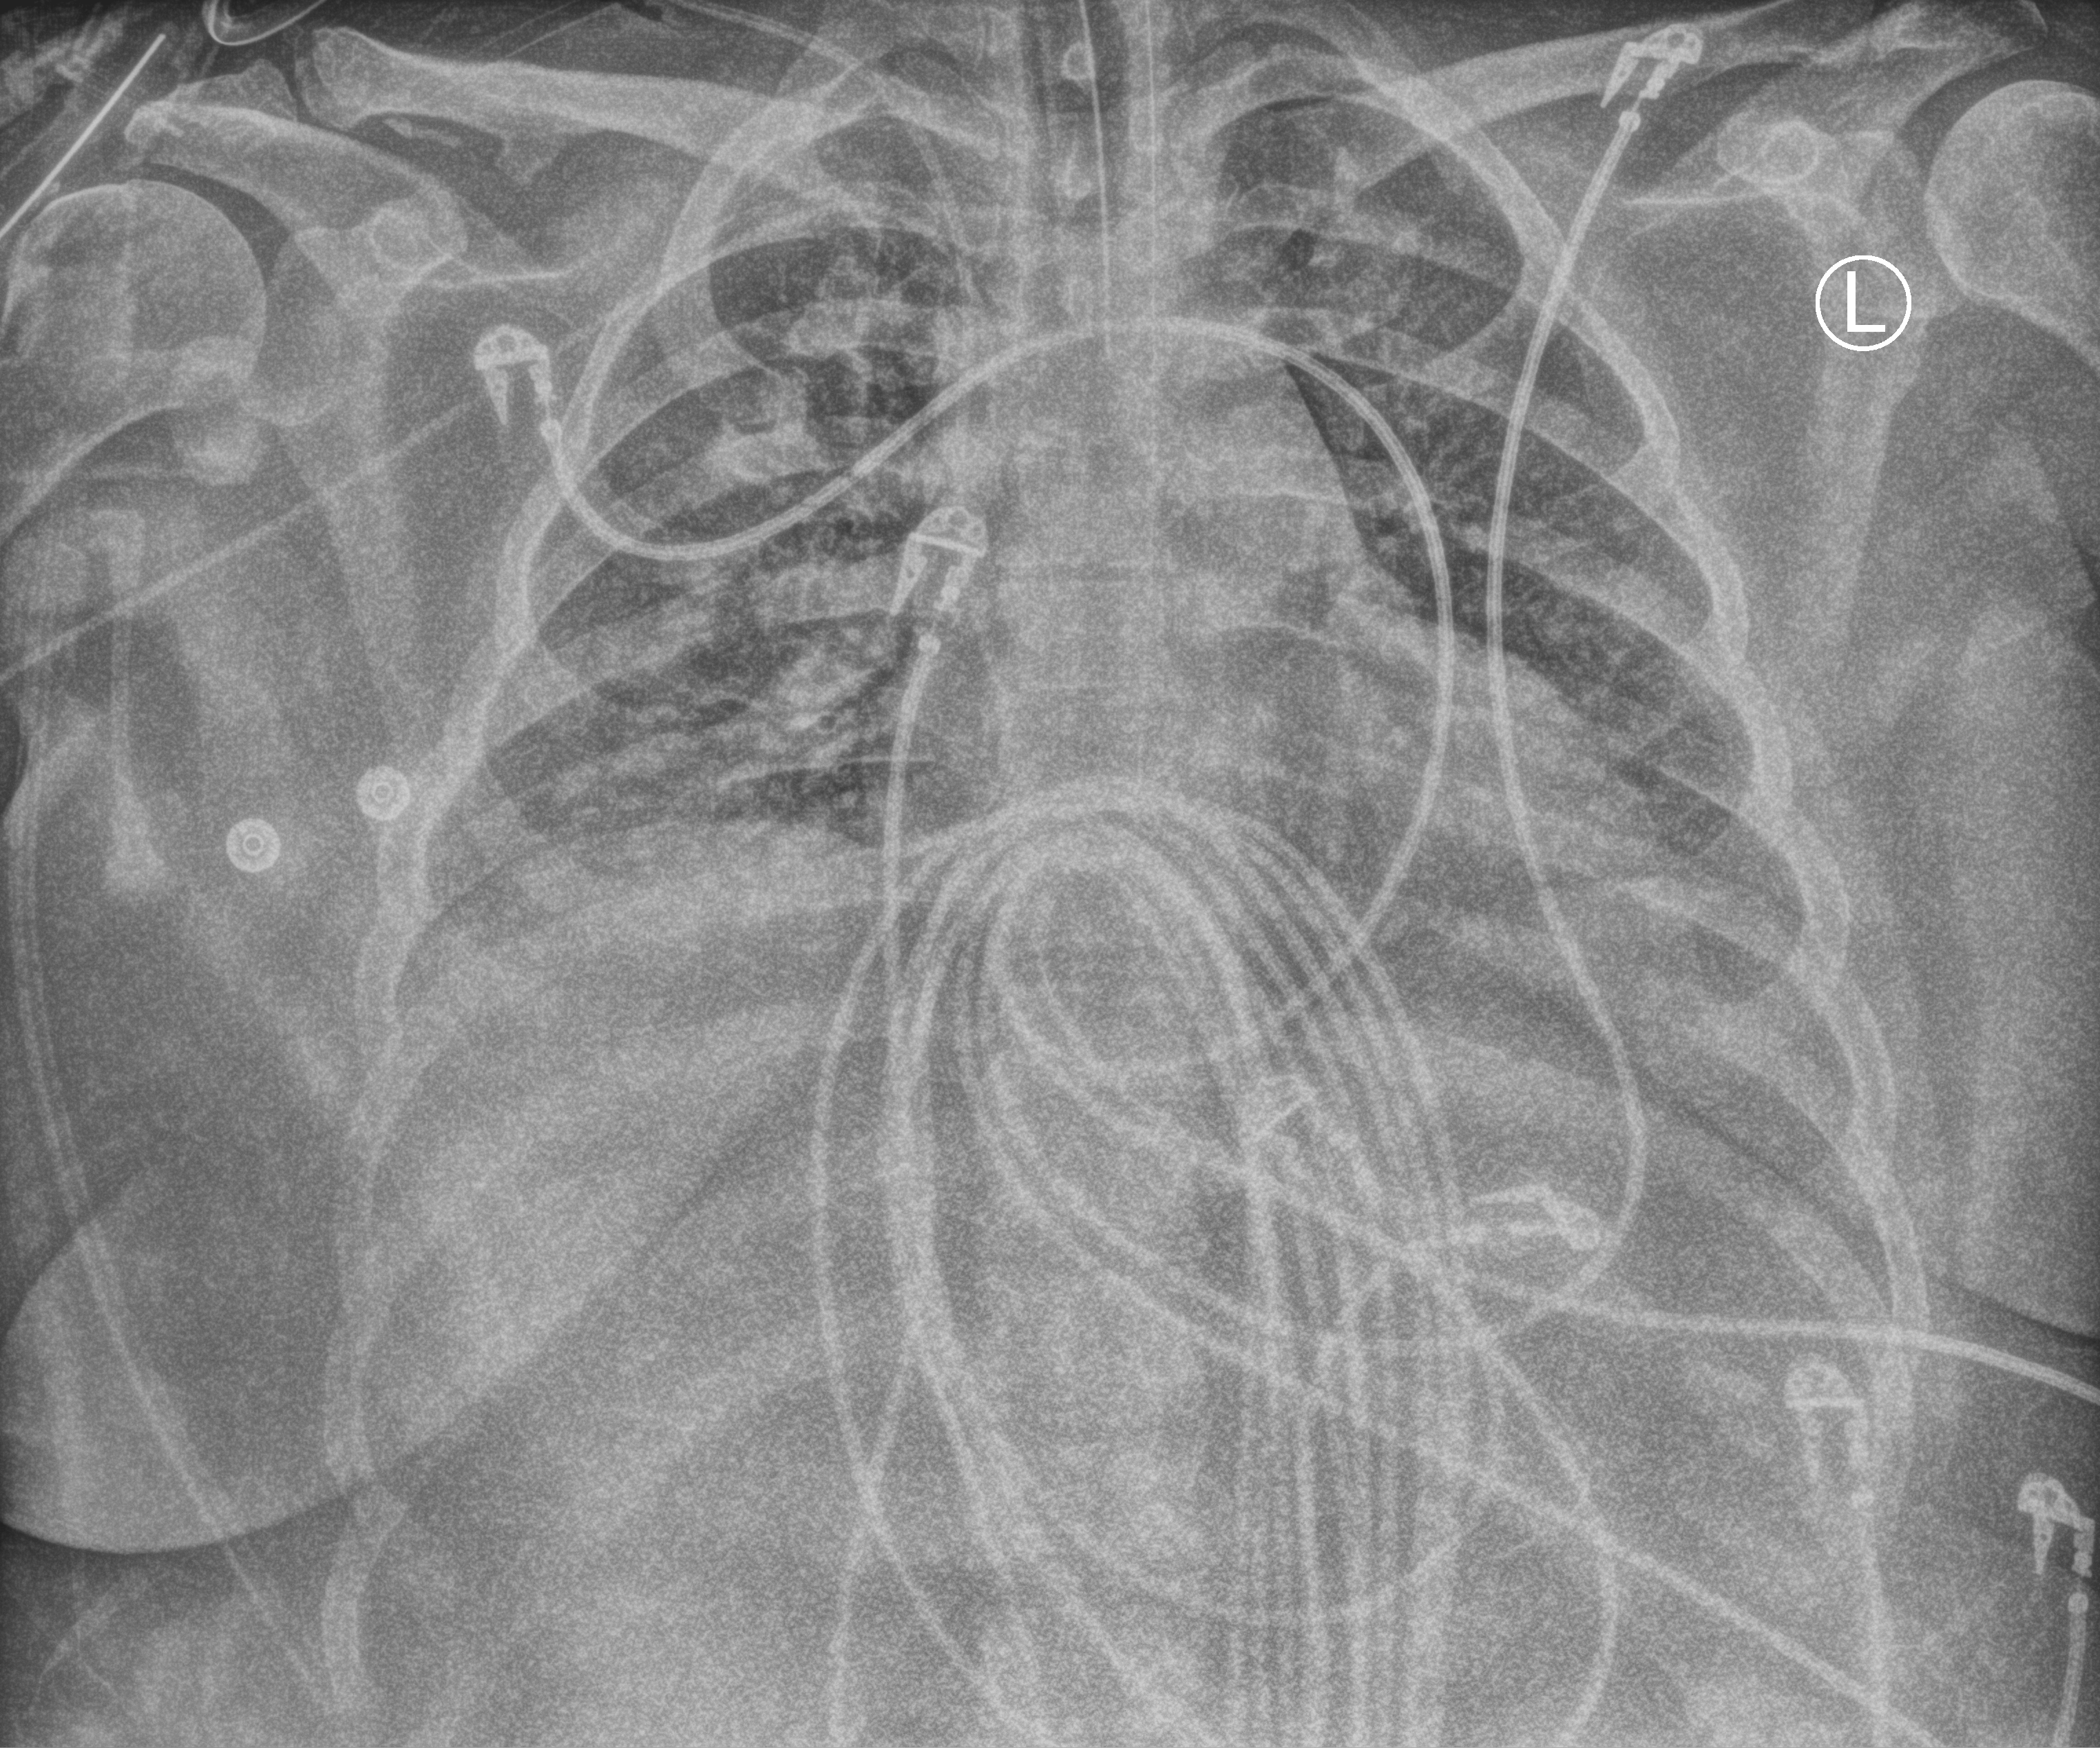
Portable chest radiograph, anteroposterior (AP) projection. Female patient hospitalised with COVID-19, age 18–59 years.
From the hospital-stay record, not from the radiograph (when in the stay this image was taken is not recorded):
- mechanically ventilated during this hospital stay: yes
- admitted to intensive care during this hospital stay: yes